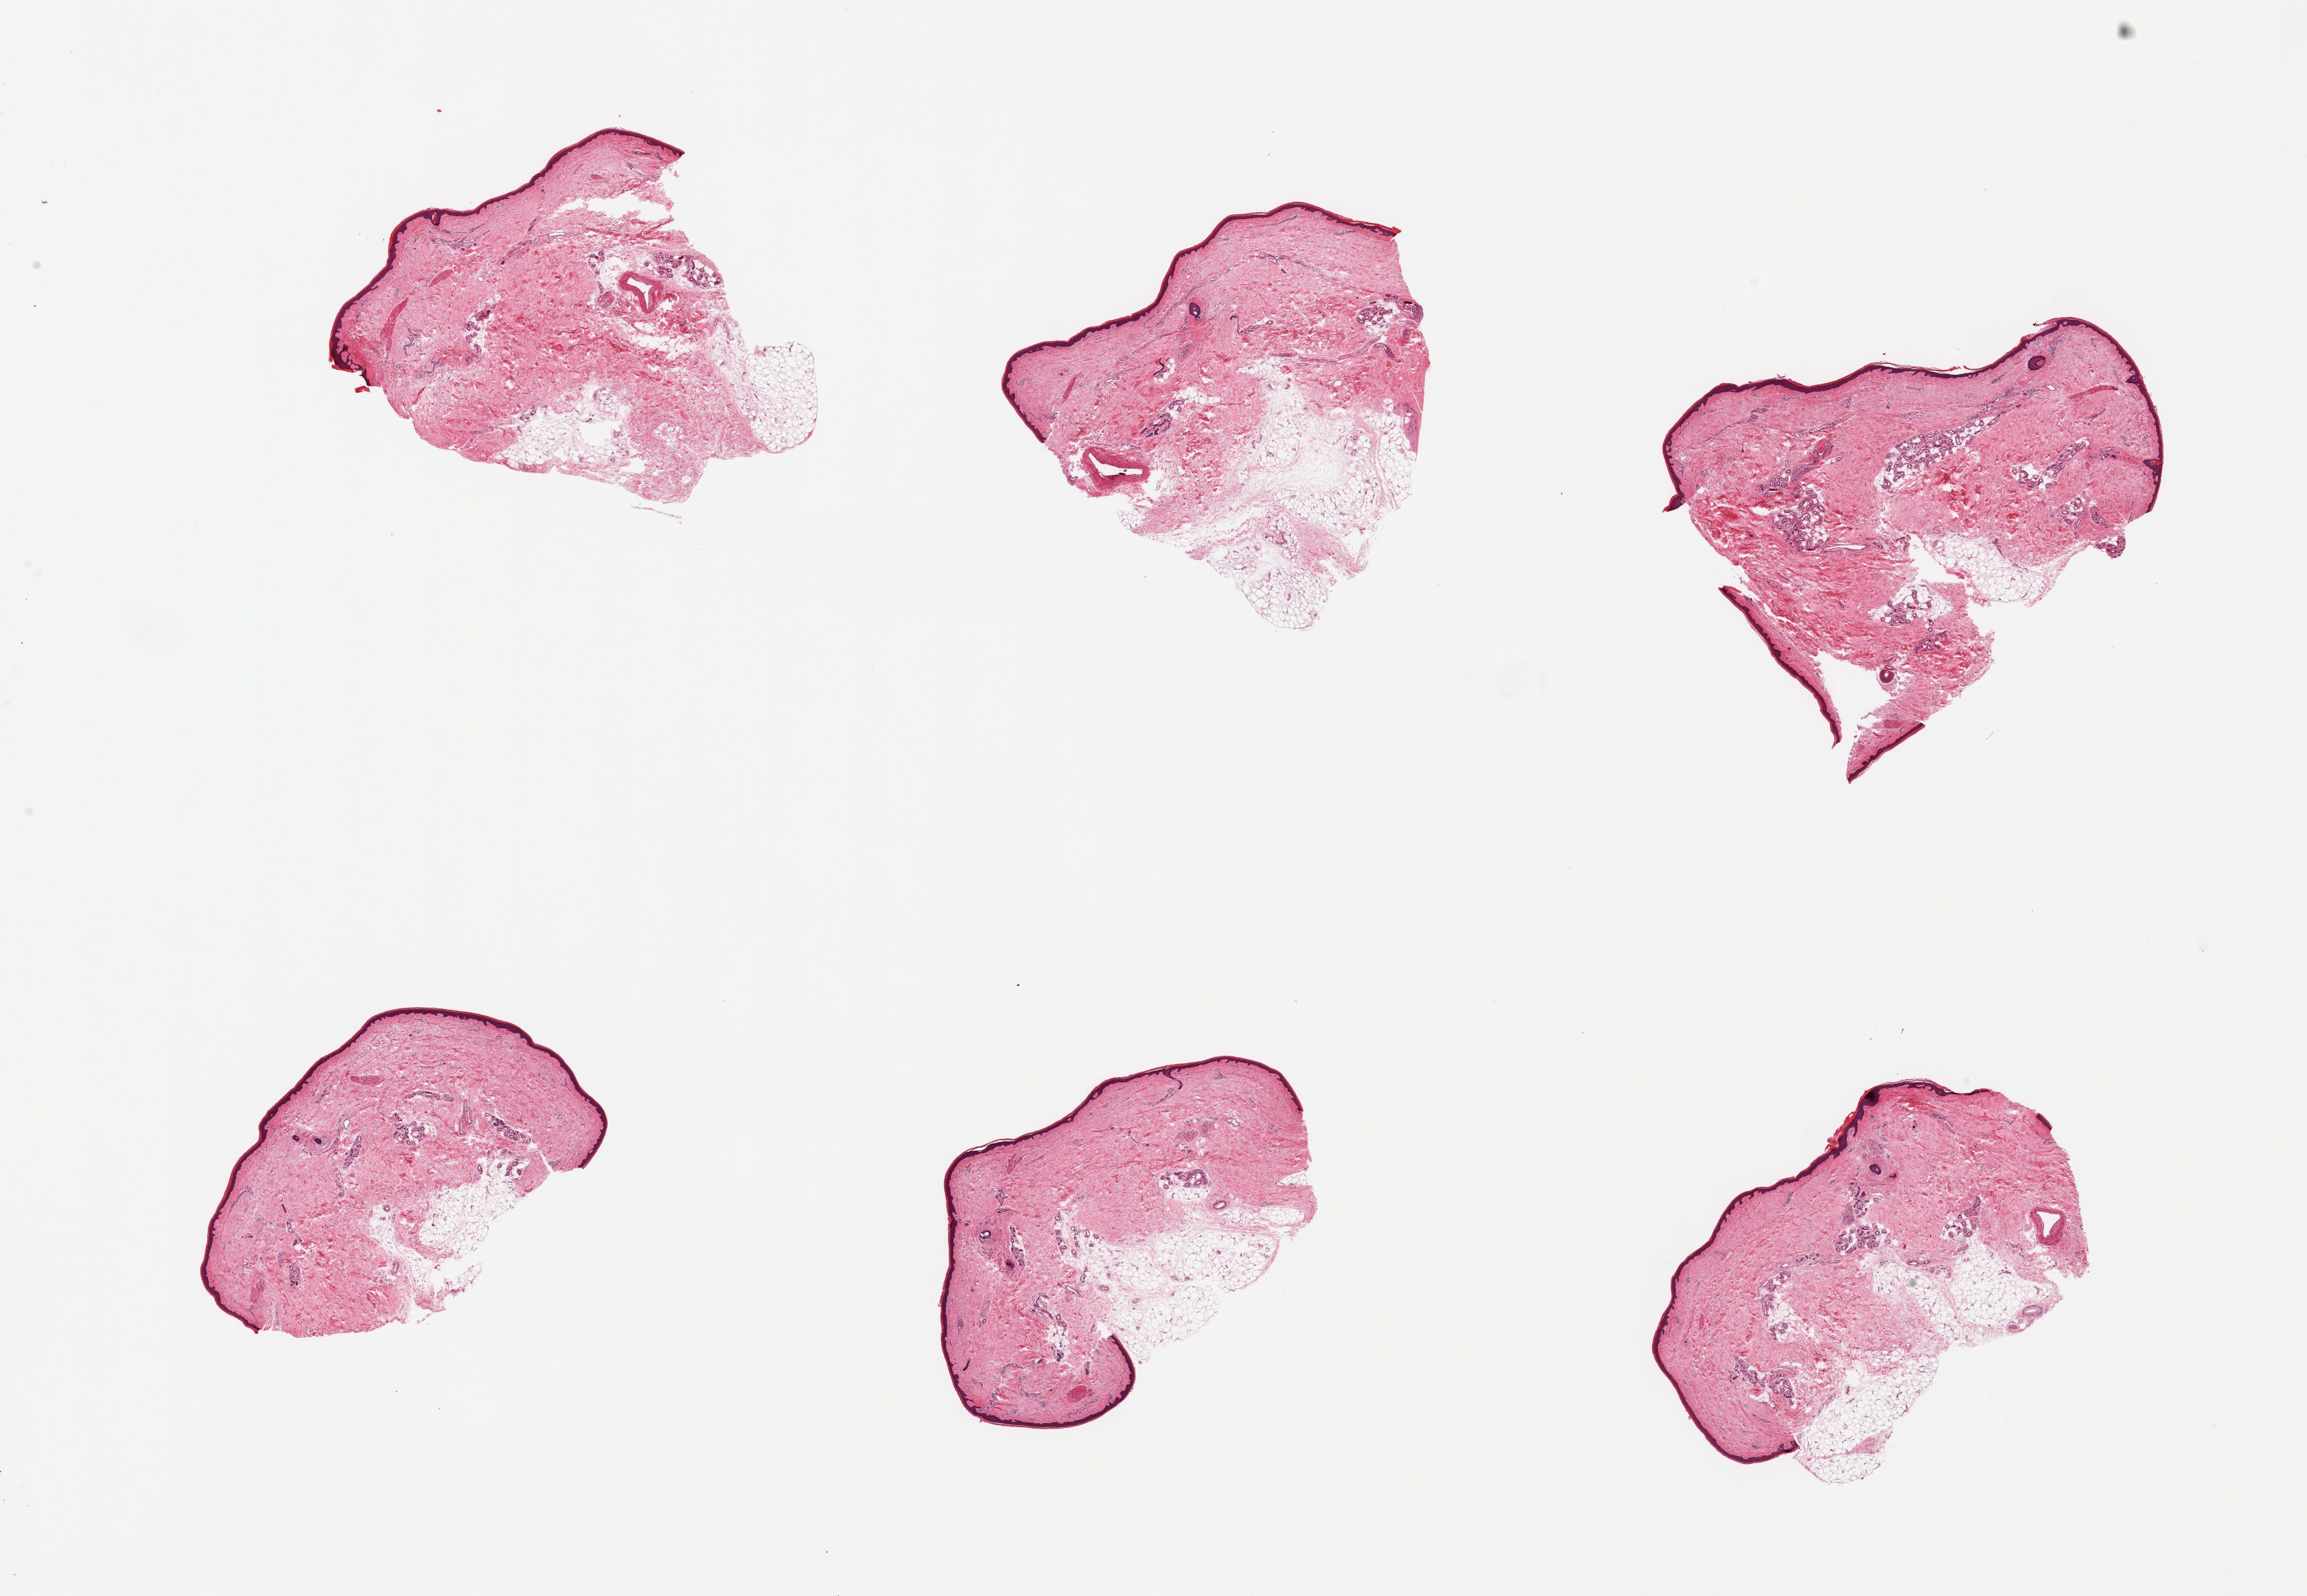
Haematoxylin and eosin whole-slide image, shown as a low-resolution overview of the whole scanned area (about 26.6 x 18.4 mm), PAXgene-fixed, paraffin-embedded tissue, sampled site (target tissue): skin of lower leg, donor tissue sample.
Reviewer comment on this tissue sample: 6 pieces; subcutaneous fat up to 1.6 mm thick; up to 10% dermal fat.